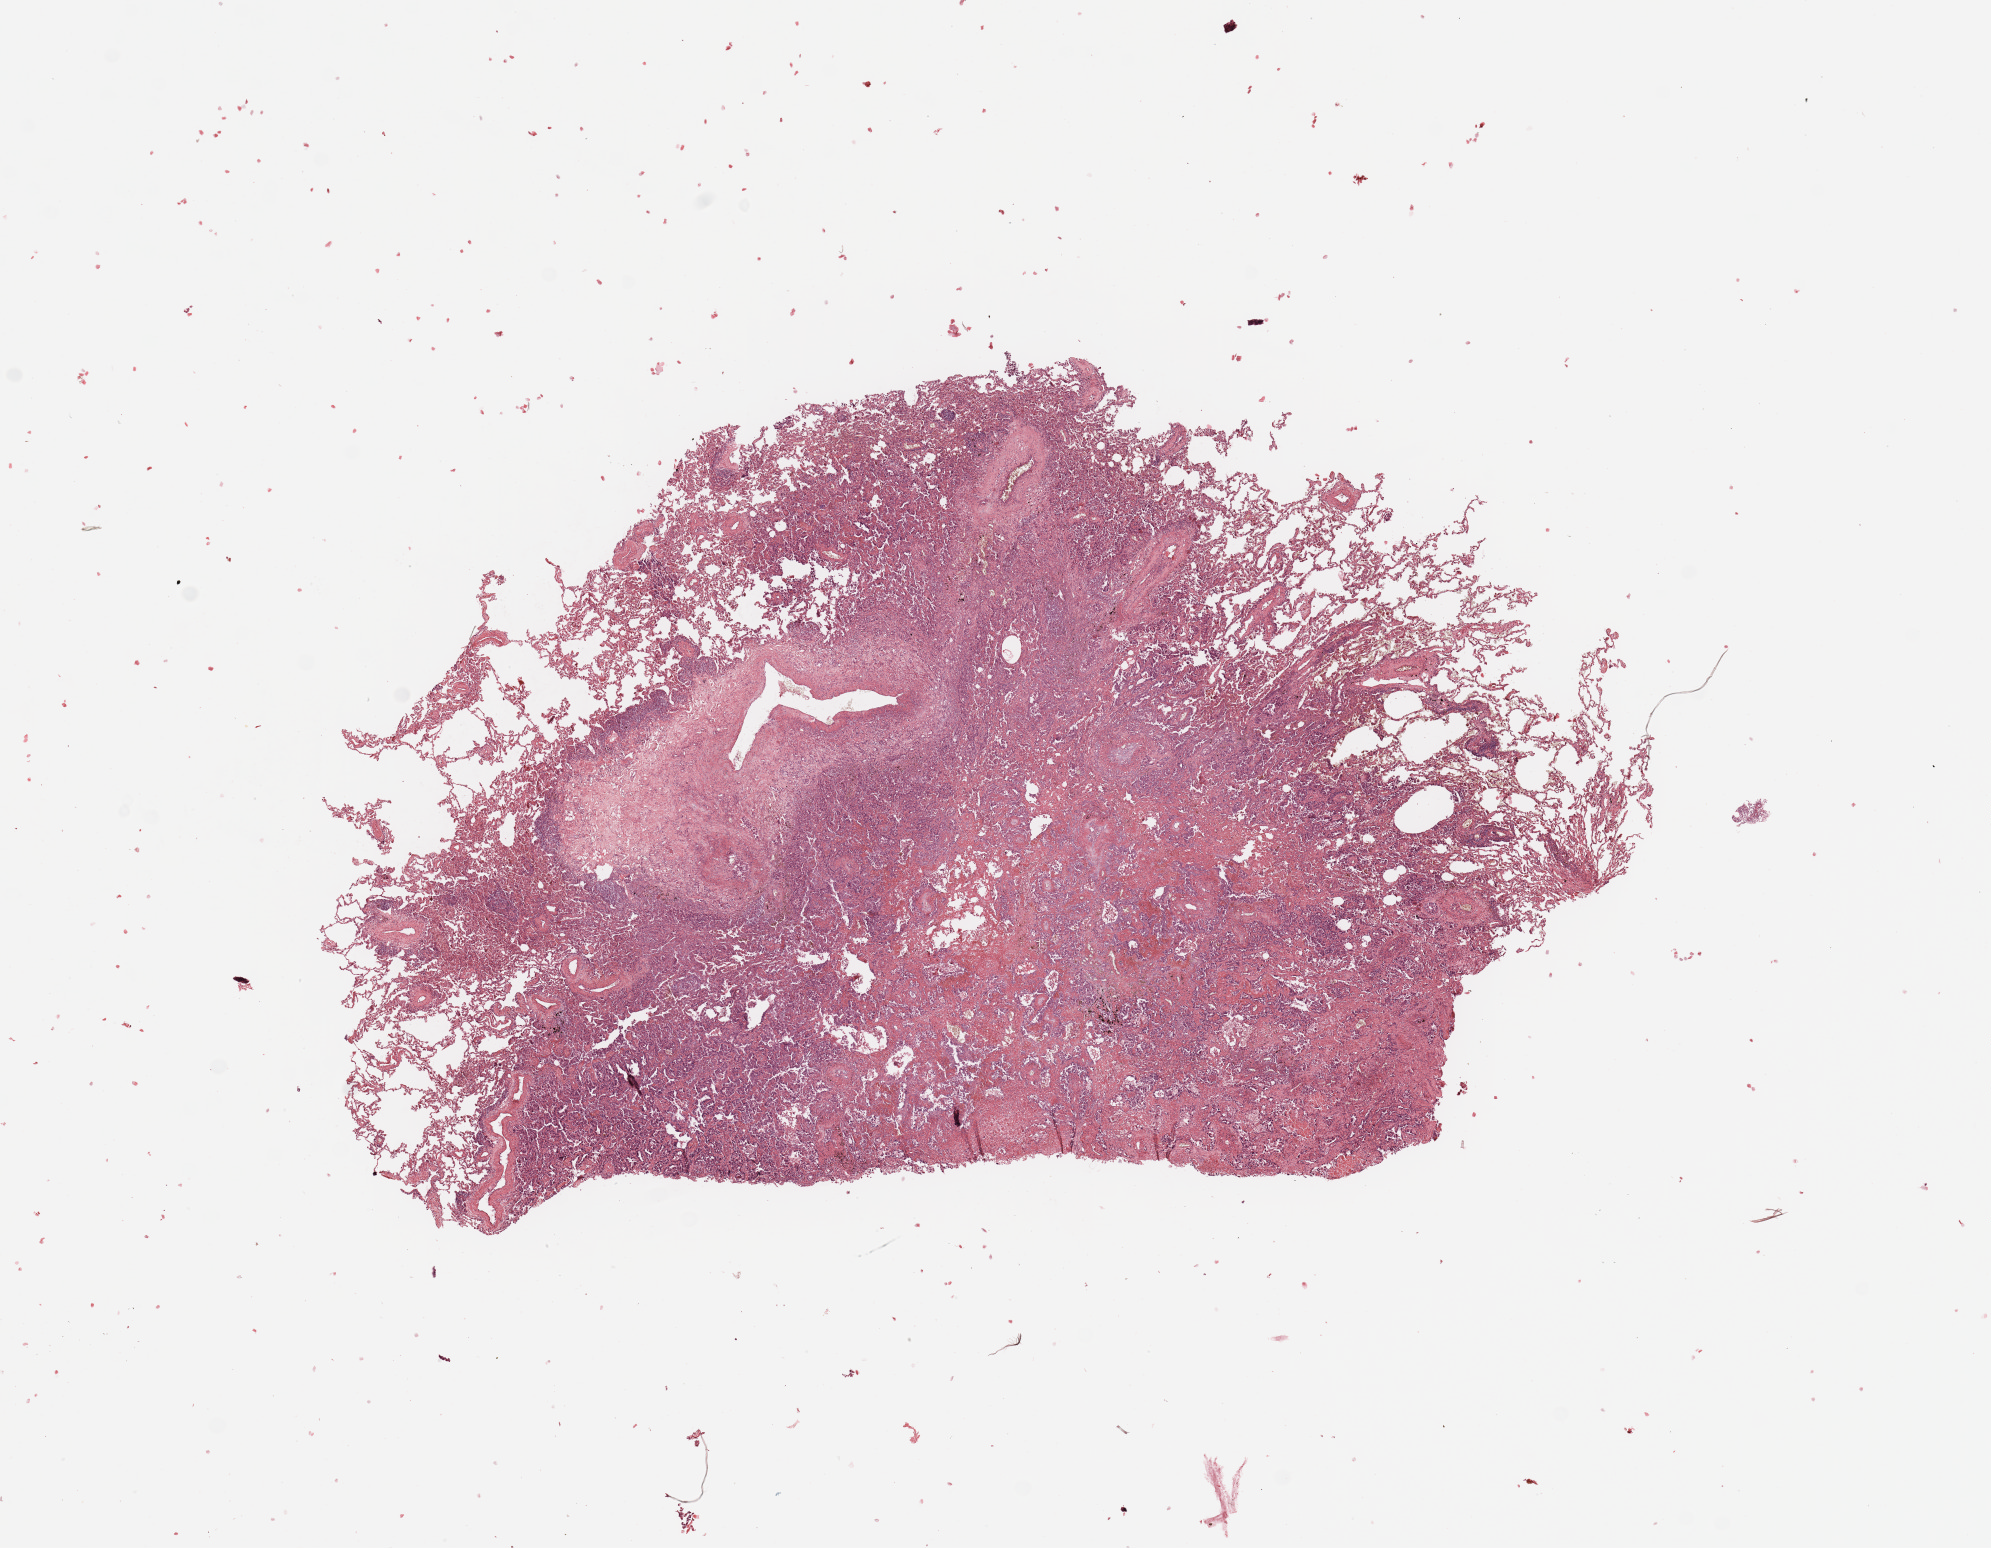
H&E whole-slide image — a low-resolution overview of the entire scanned area, about 15.8 x 12.2 mm (acquisition: 20x scan), tumour tissue sample, sampled site: lung. Patient: male, age 69 years.
Histologic diagnosis: Adenocarcinoma, NOS.